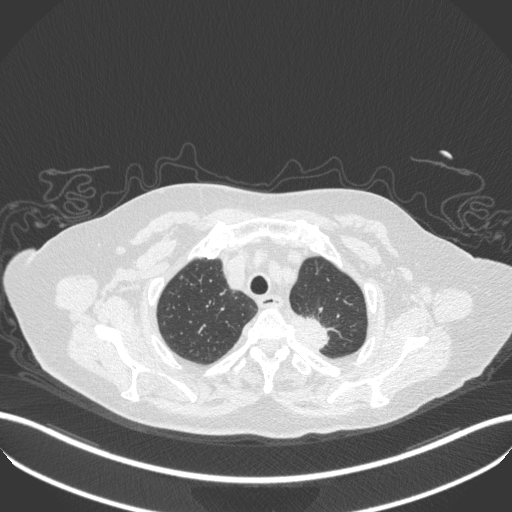
Chest CT, one axial slice. Slice 291 of 353 in the series (ordered by position). Reconstruction kernel B31f. Lung window (W 1500 / L -600 HU). 1 mm slice thickness. 512 × 512 image matrix, field of view 400 × 400 mm. Patient: female, 81 years. Case-level facts recorded for this patient, not image findings: clinical TNM (as recorded): T2a N0 M0.
Annotated regions visible in this slice (rectangle marked by the reading radiologist):
- lung tumour (recorded histology: adenocarcinoma): bounding box <284,305,337,356> (left, top, right, bottom; pixels)